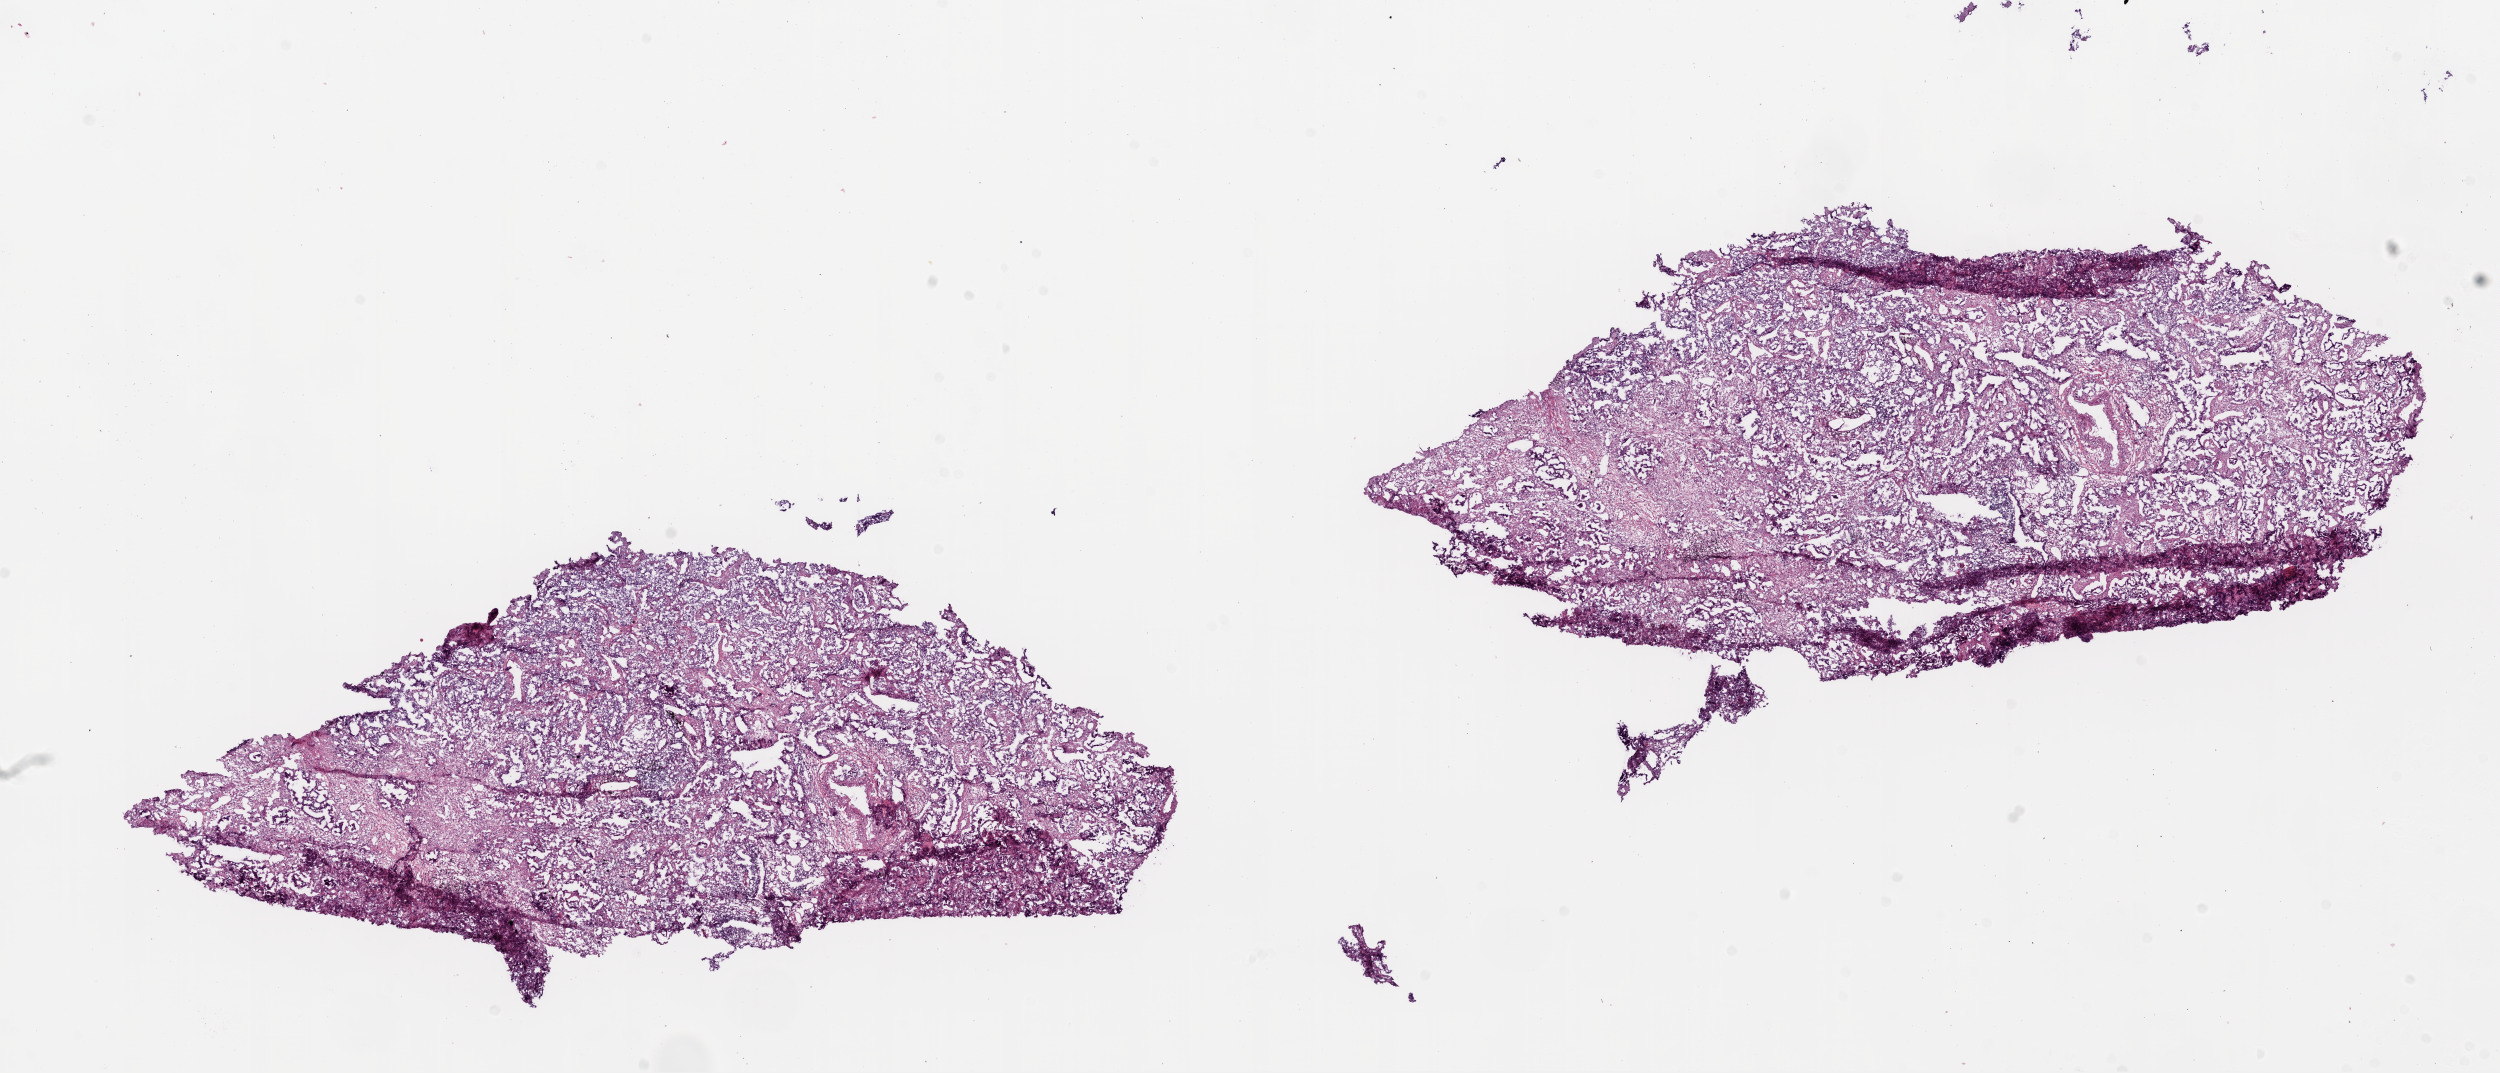
Digitized H&E tissue section (whole slide) — a low-resolution overview of the entire scanned area, about 20.1 x 8.6 mm (from a 20x scan). Frozen section. Sample: primary tumour, lung. Female patient; age at initial diagnosis 45 years. Slide review estimates, as recorded: tumour cells 80%, tumour nuclei 70%, normal cells 0%, stromal cells 20%, necrosis 0%.
TNM: T3 N2 M0. Pathologic diagnosis: Adenocarcinoma, NOS (upper lobe, lung). AJCC pathologic stage: IIIA.